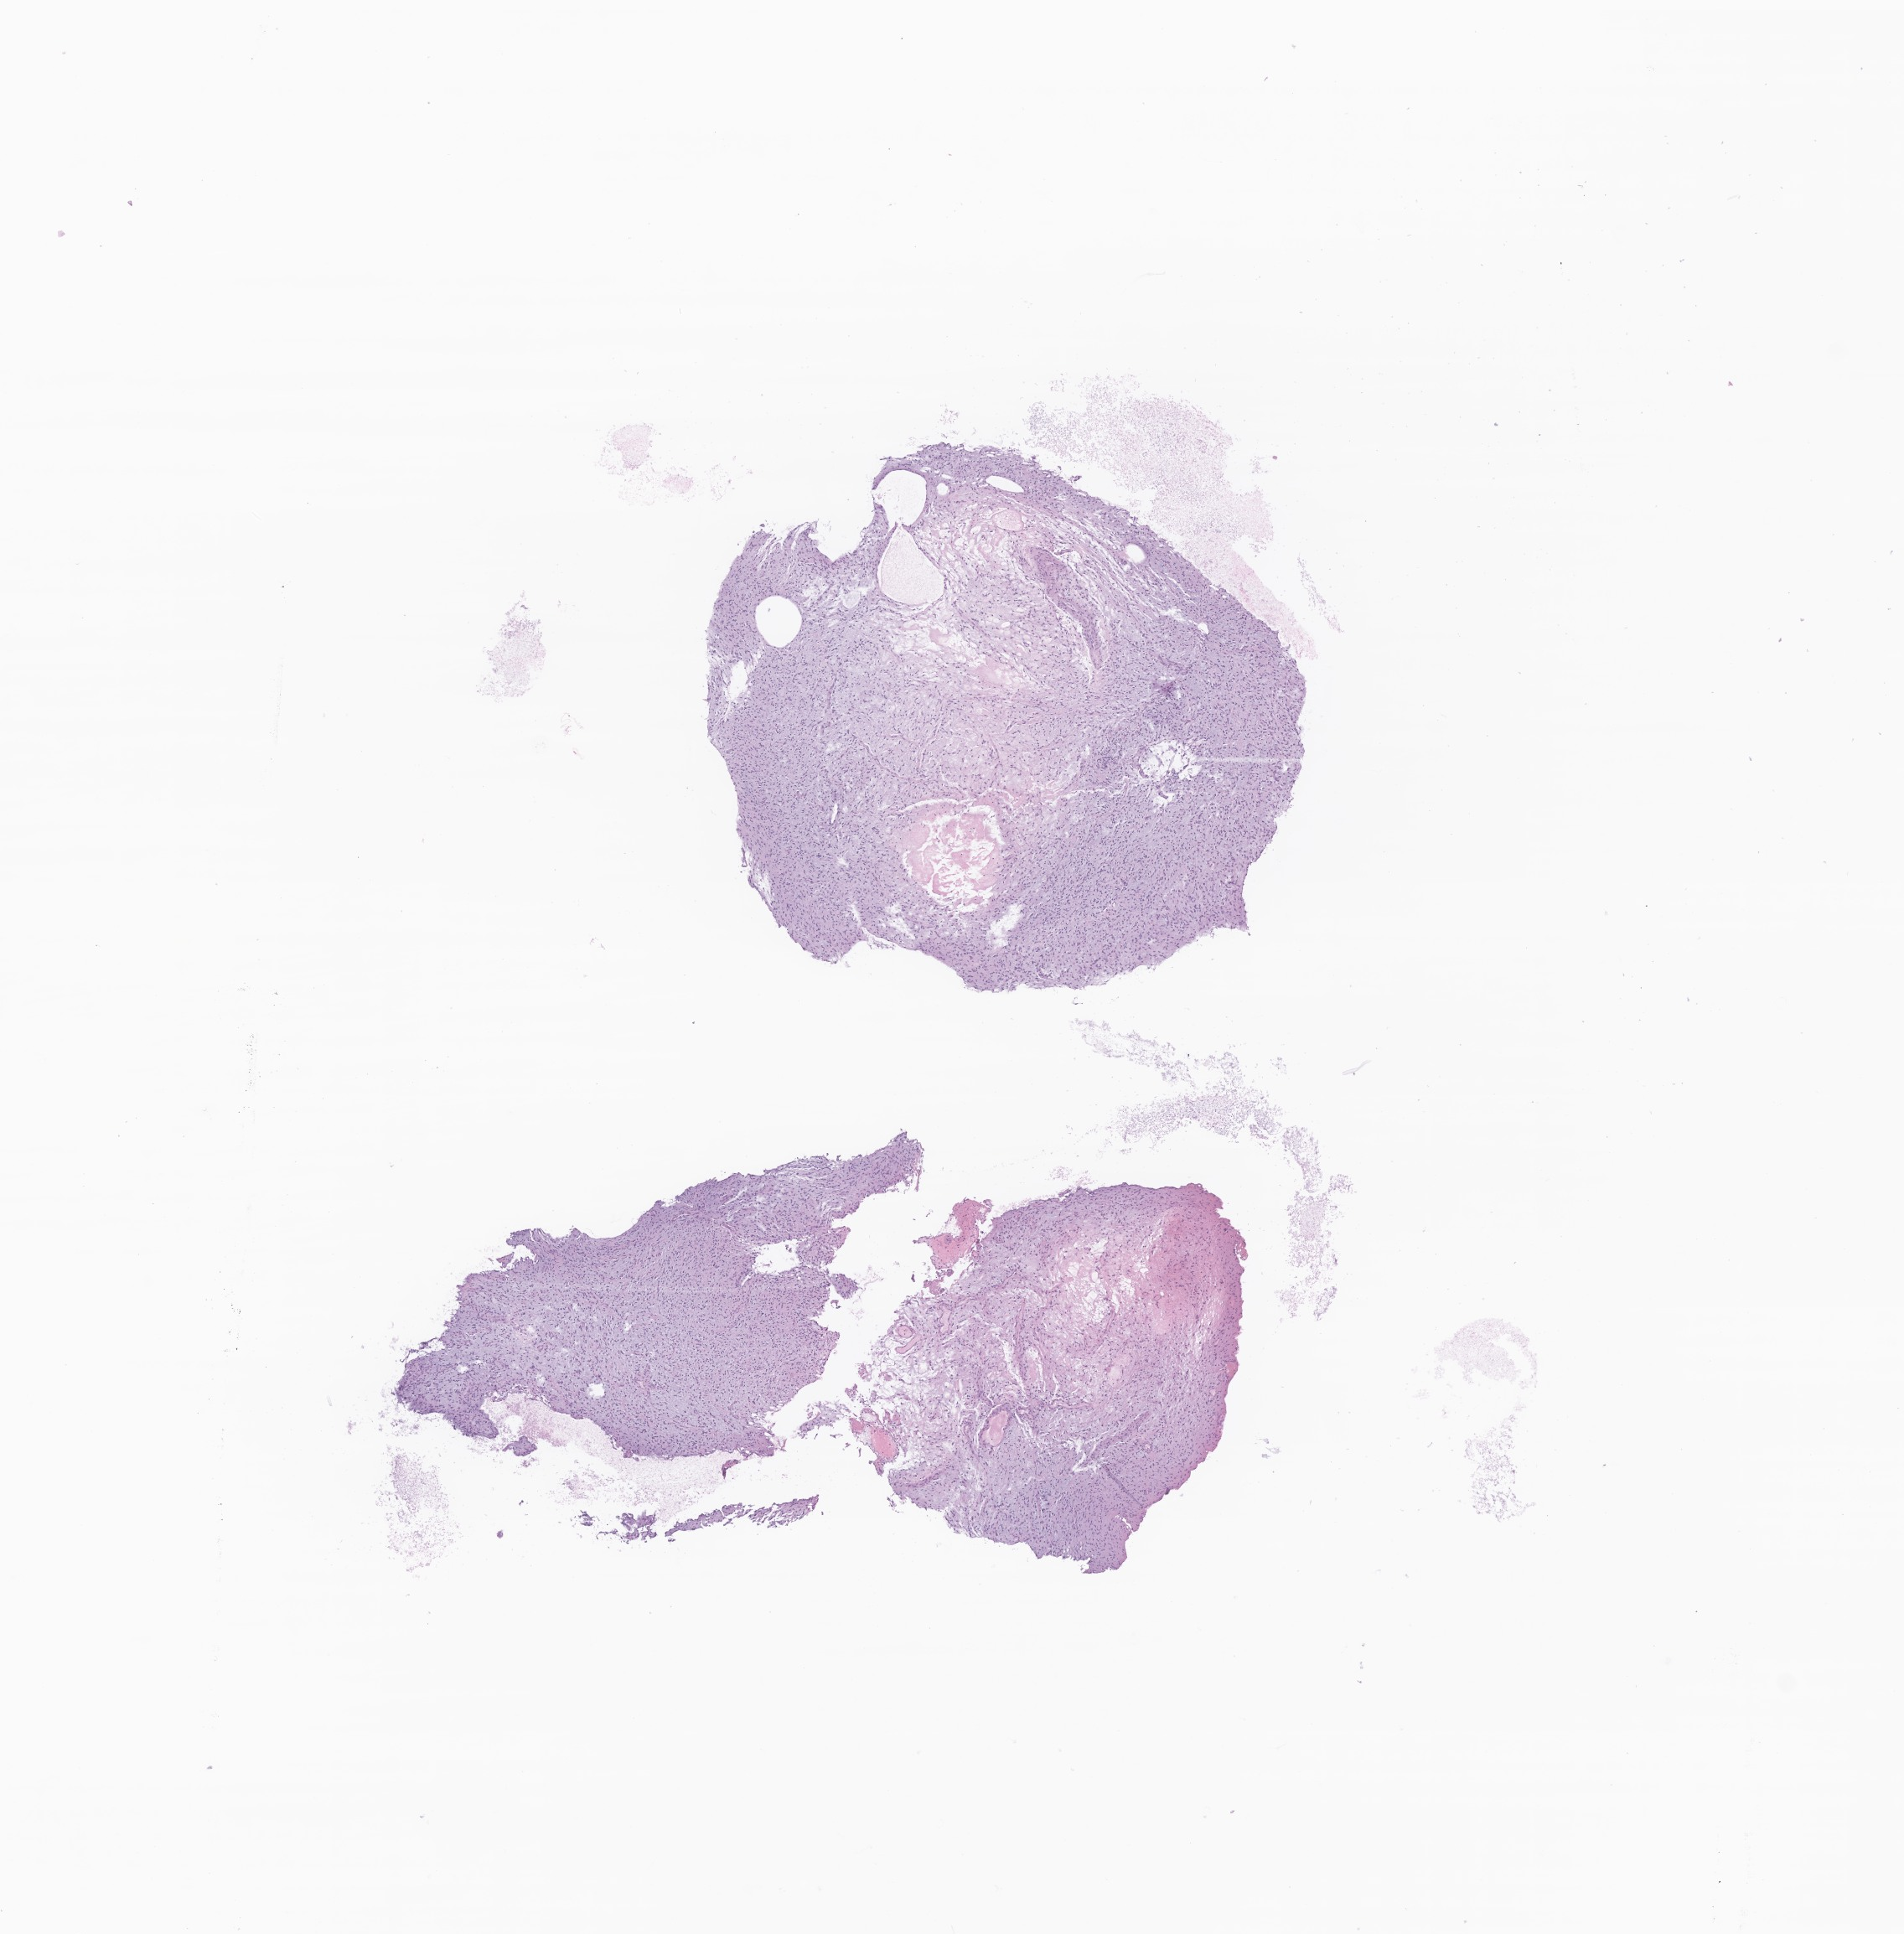
H&E whole-slide image of tumor tissue from the brain — a low-resolution overview of the entire scanned area, about 9.6 x 9.7 mm; FFPE section. Male patient, age 401 days (about 1.1 years).
Recorded diagnosis: Astrocytoma, NOS.